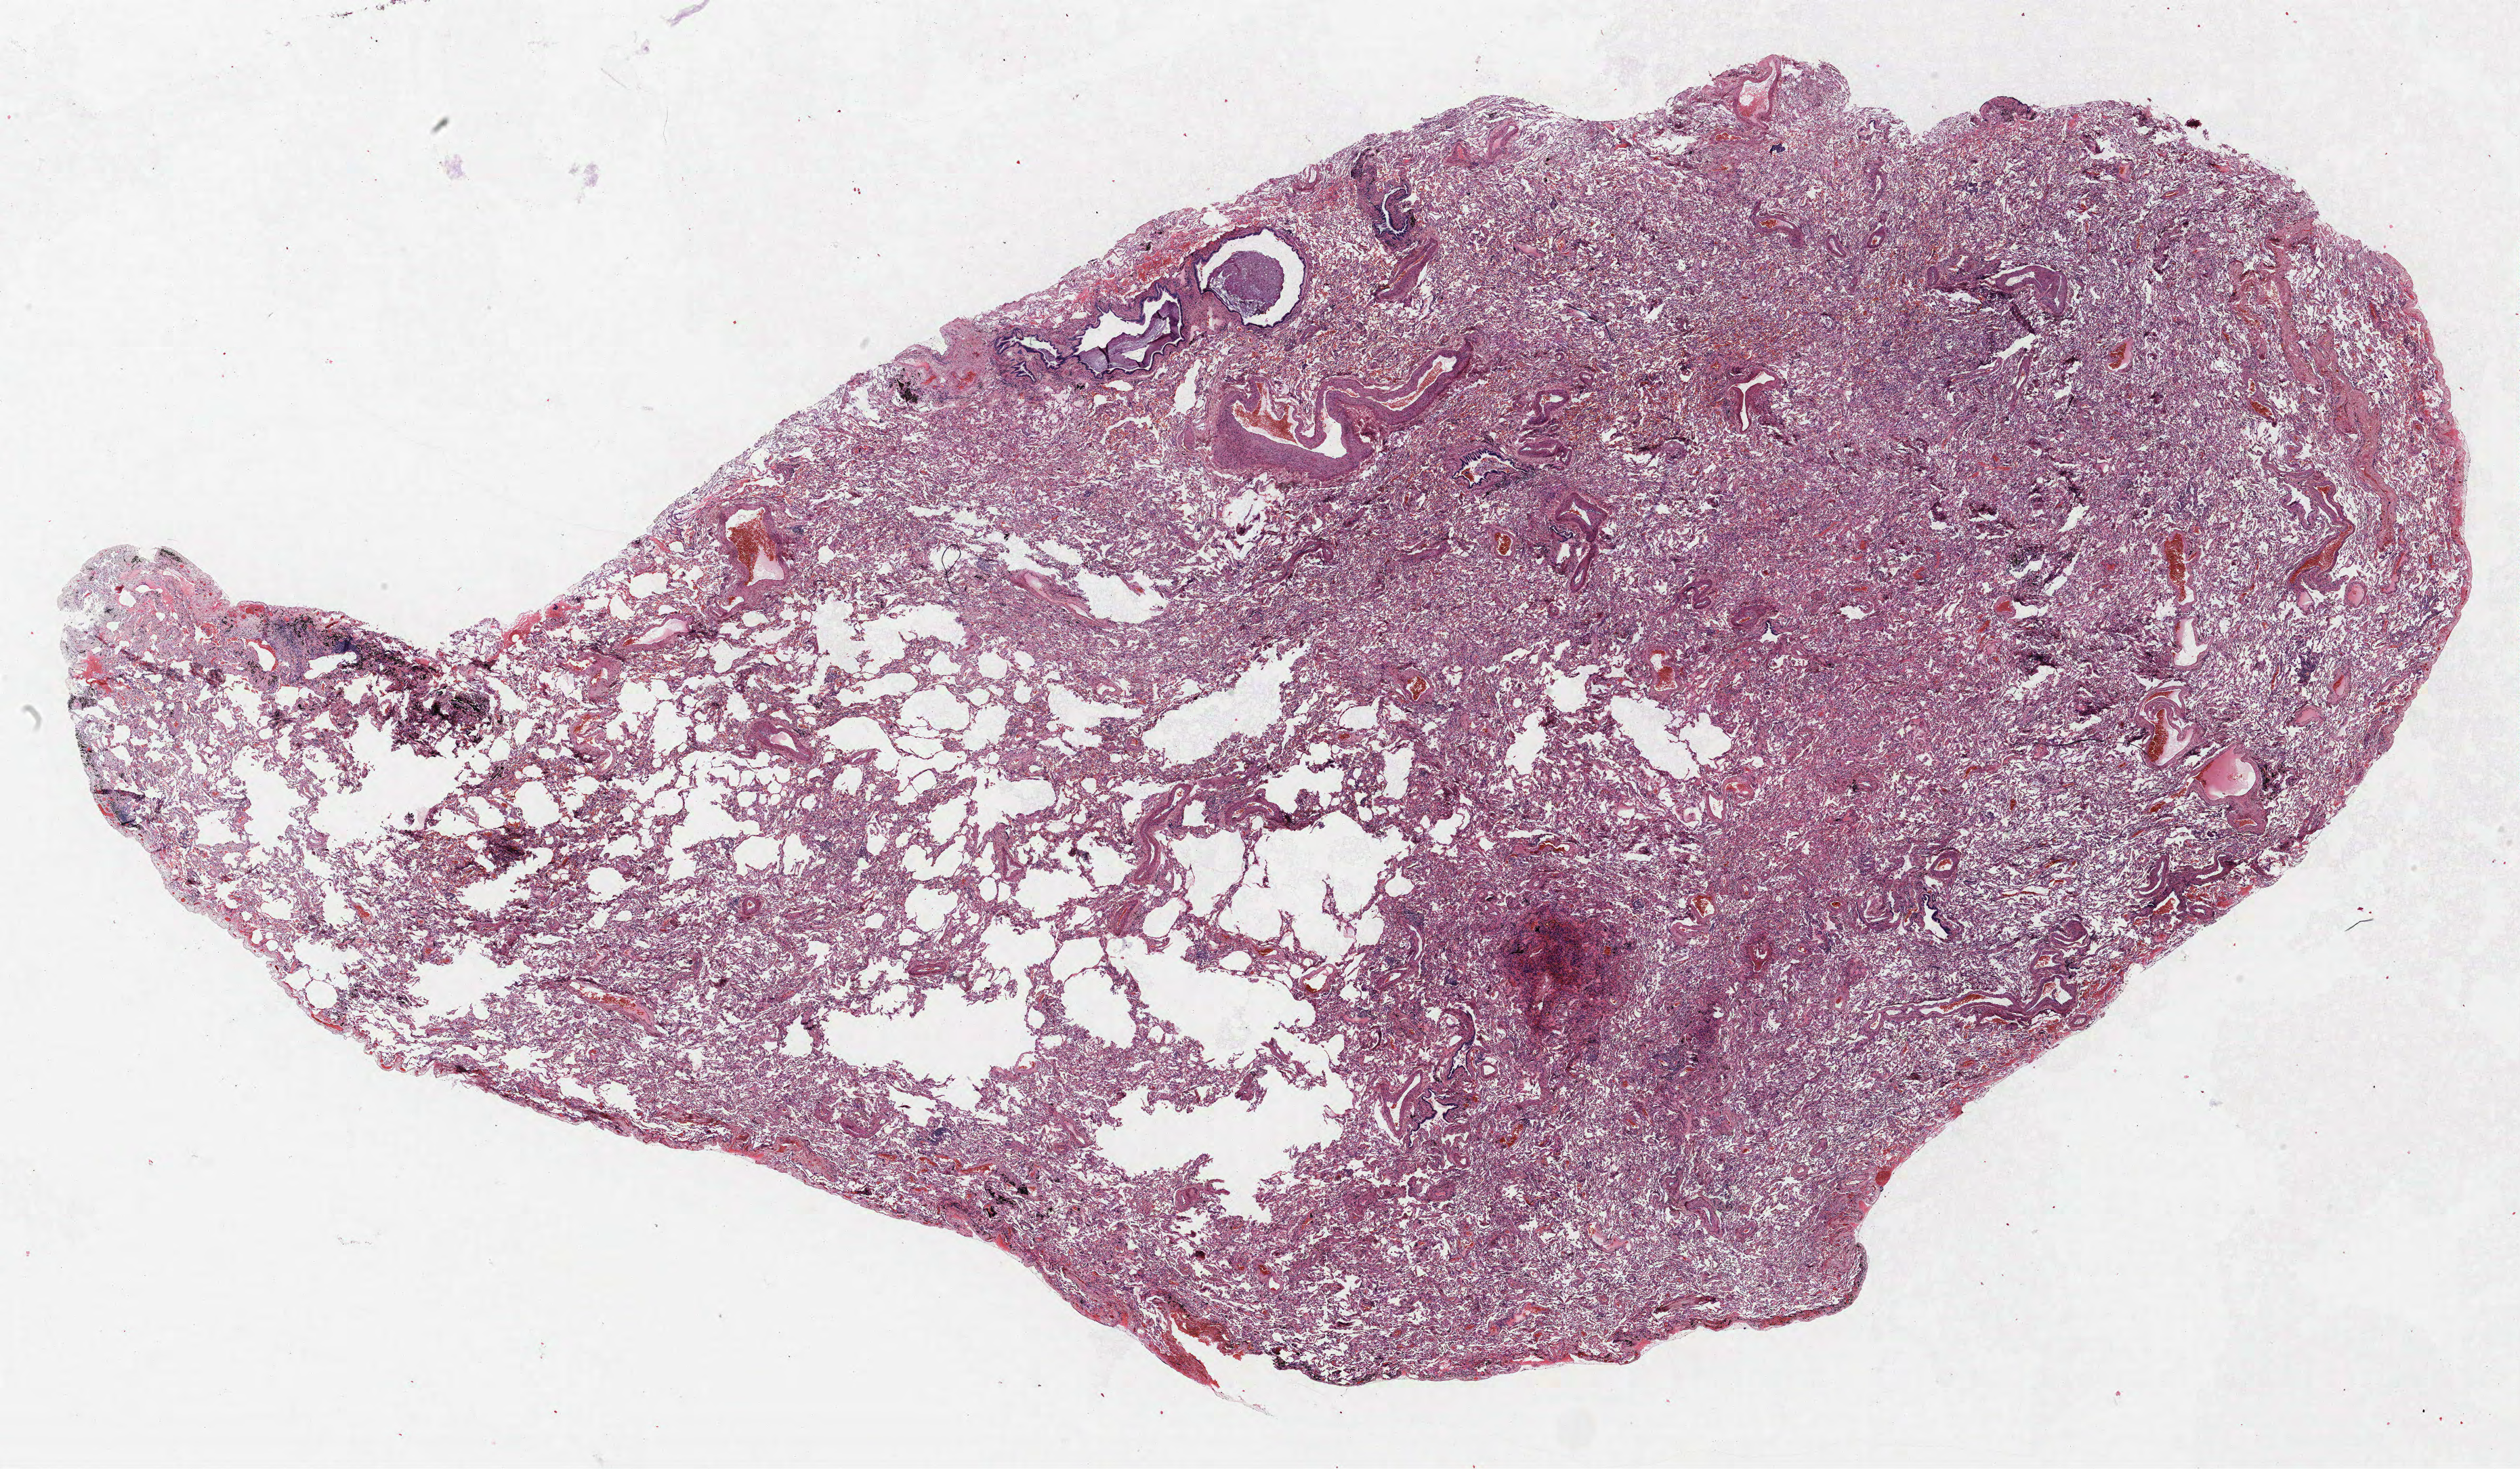
H&E whole-slide image — shown as a low-resolution overview of the whole scanned area (about 29.8 x 17.3 mm, from a 40x scan). FFPE section. Lung tissue. Male, age 67 at enrolment. Former smoker at enrolment.
Participant's lung-cancer diagnosis: Squamous cell carcinoma, NOS (ICD-O-3 8070/3).